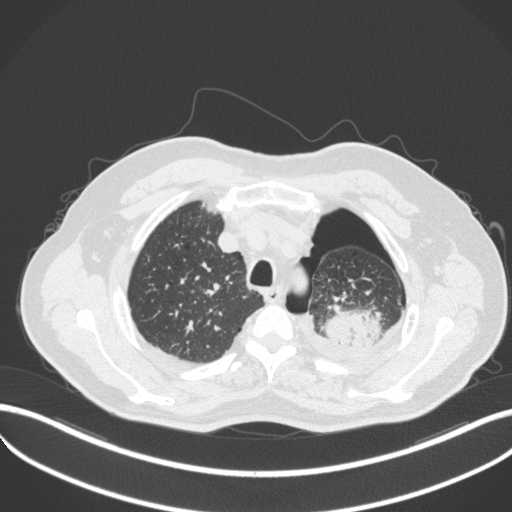
Chest CT, one axial slice. Position 411 of 466 along the scan axis. Reconstruction kernel B31f. 120 kVp. Lung window (W 1500 / L -600 HU). 1 mm slice thickness. 512 × 512 image matrix, field of view 400 × 400 mm. Male patient, age 76 years. From the clinical record (not read from this slice): clinical TNM (as recorded): T3 N0 M1b.
Annotated regions visible in this slice (rectangle marked by the reading radiologist):
- lung tumour (recorded histology: adenocarcinoma): bounding box [x1, y1, x2, y2] px = [316, 307, 387, 351]